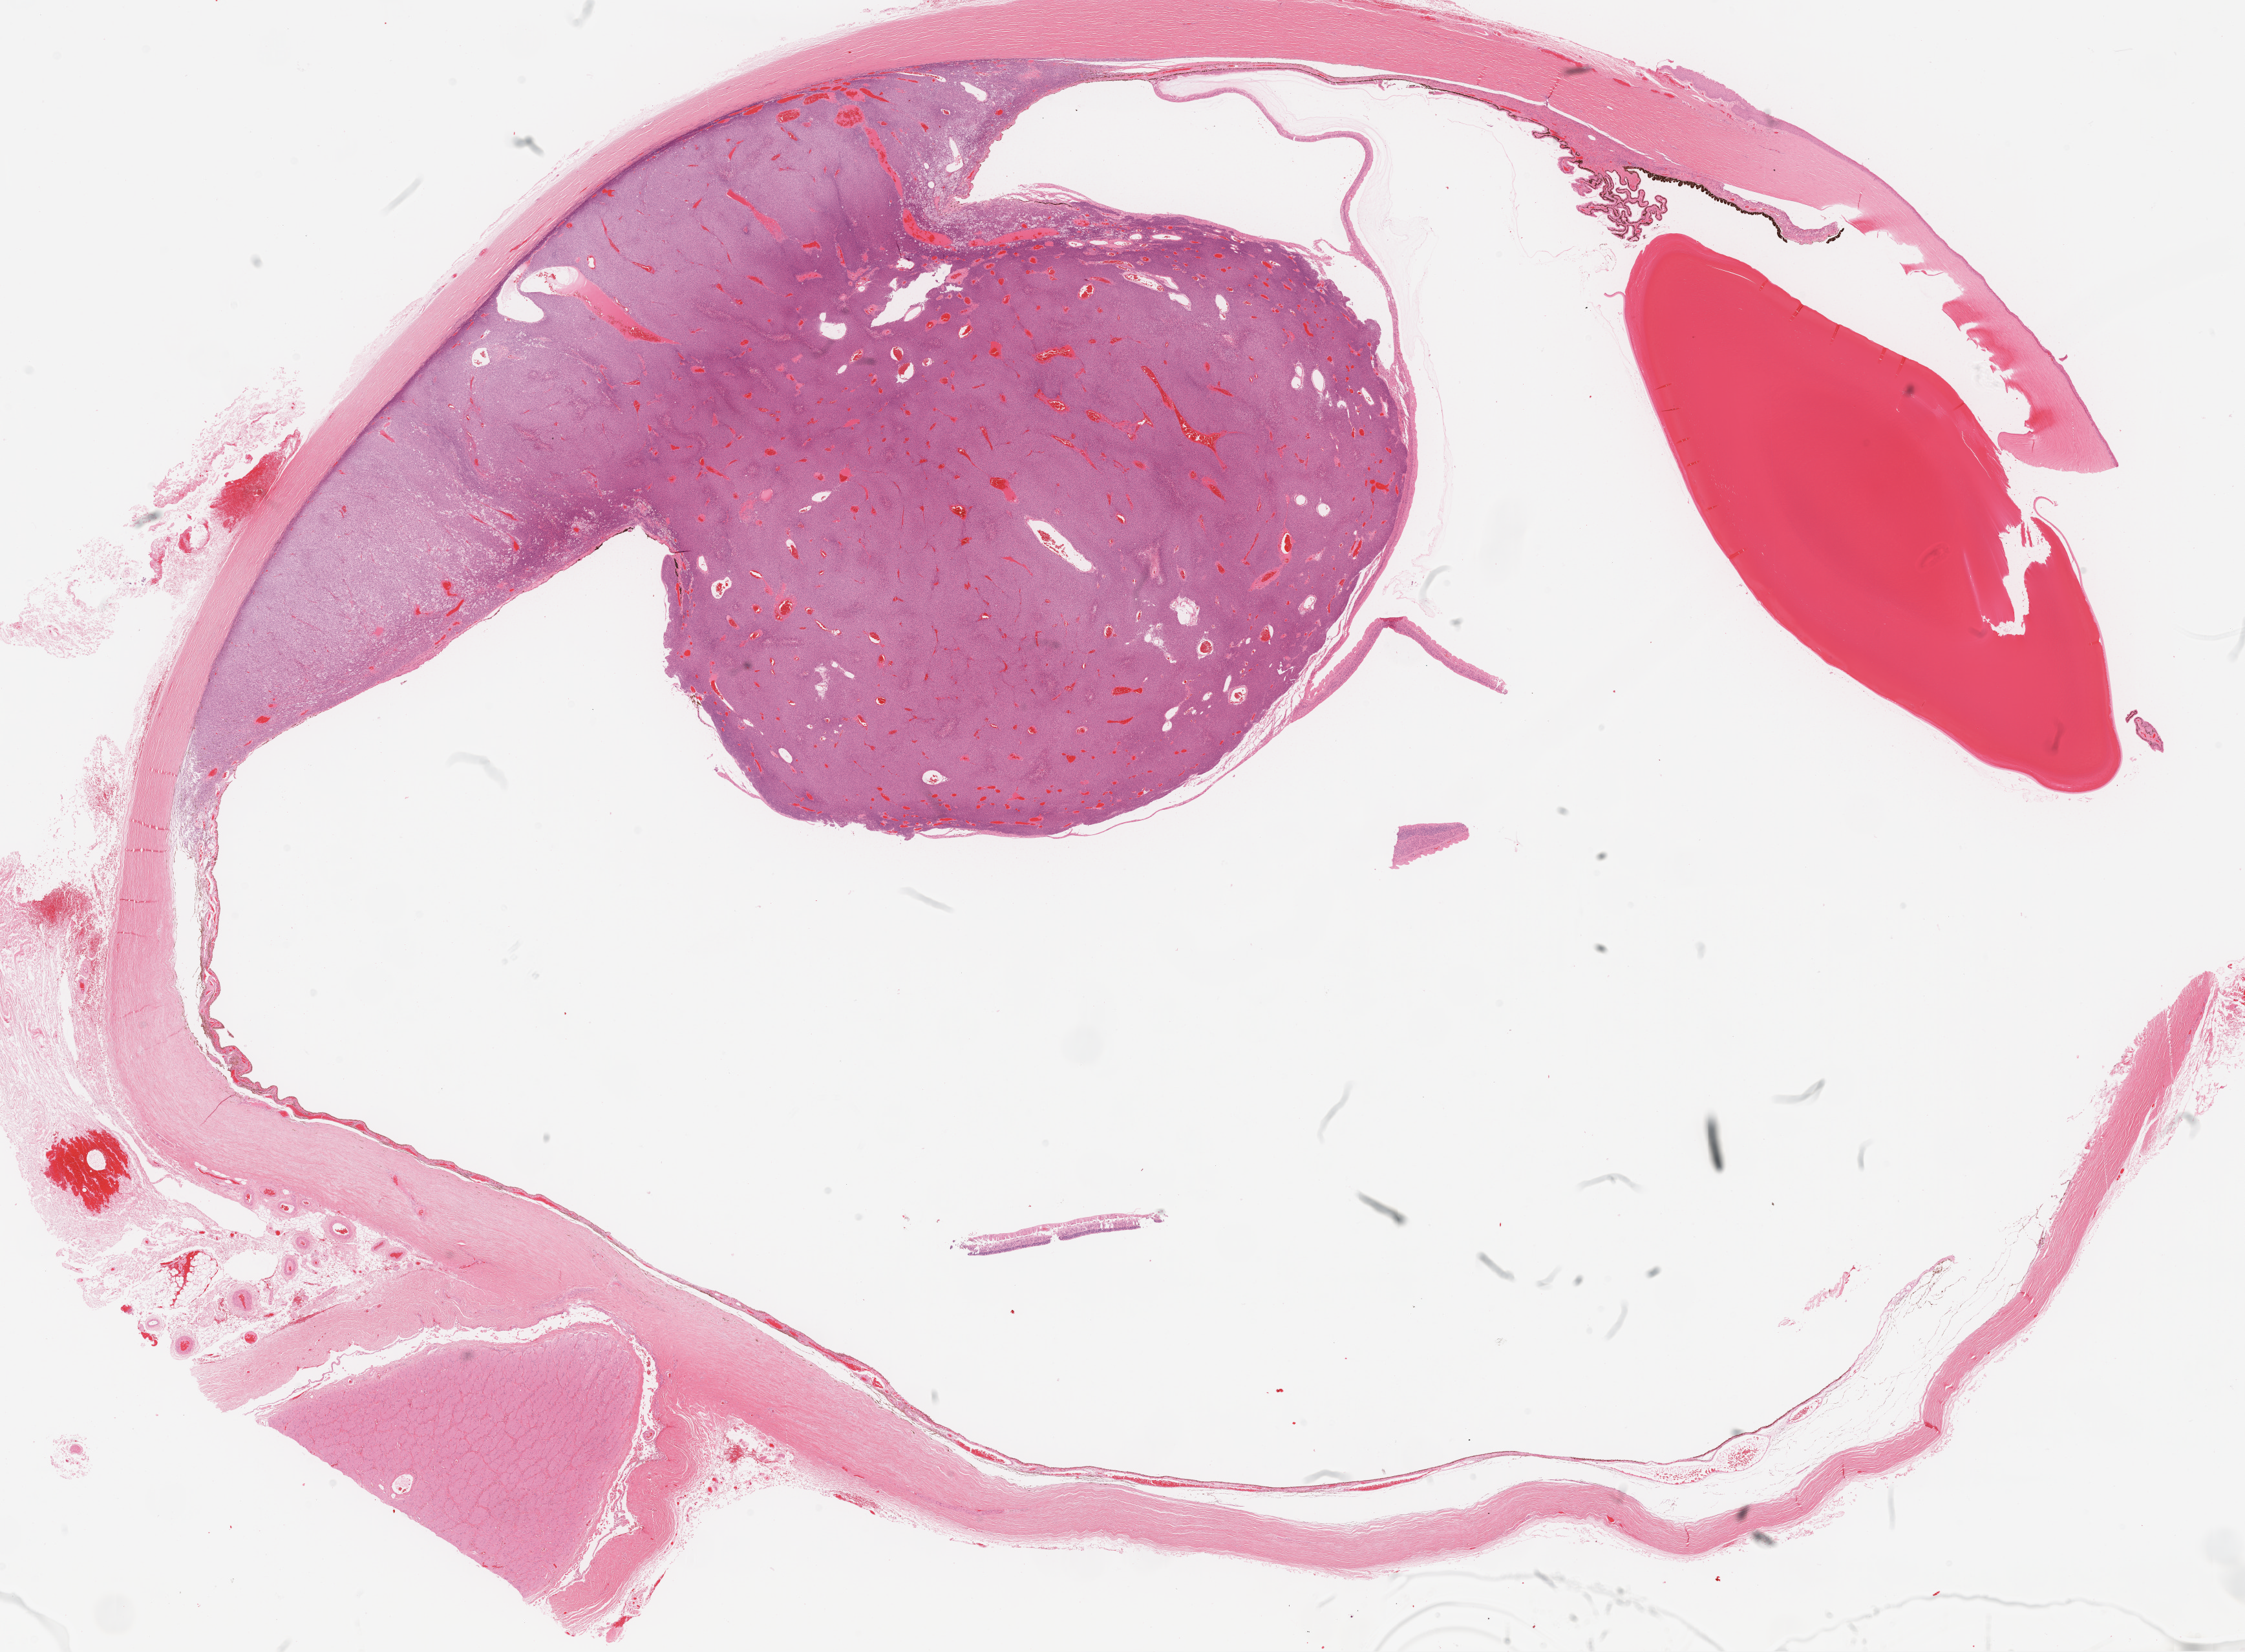
Whole-slide histology image, H&E — low-resolution overview of the scanned area, about 28.0 x 20.6 mm (from a 20x scan); FFPE section; sample: primary tumour, uvea. Male patient; age at initial diagnosis 39 years. Slide review estimates, as recorded: tumour cells 50%, tumour nuclei 60%, normal cells 50%, stromal cells 0%, necrosis 0%. Inflammatory infiltration, as recorded: lymphocyte infiltration 1%, monocyte infiltration 0%, neutrophil infiltration 0%.
AJCC pathologic stage: IIIA (7th edition). Histologic diagnosis: Spindle cell melanoma, NOS. Laterality: left.